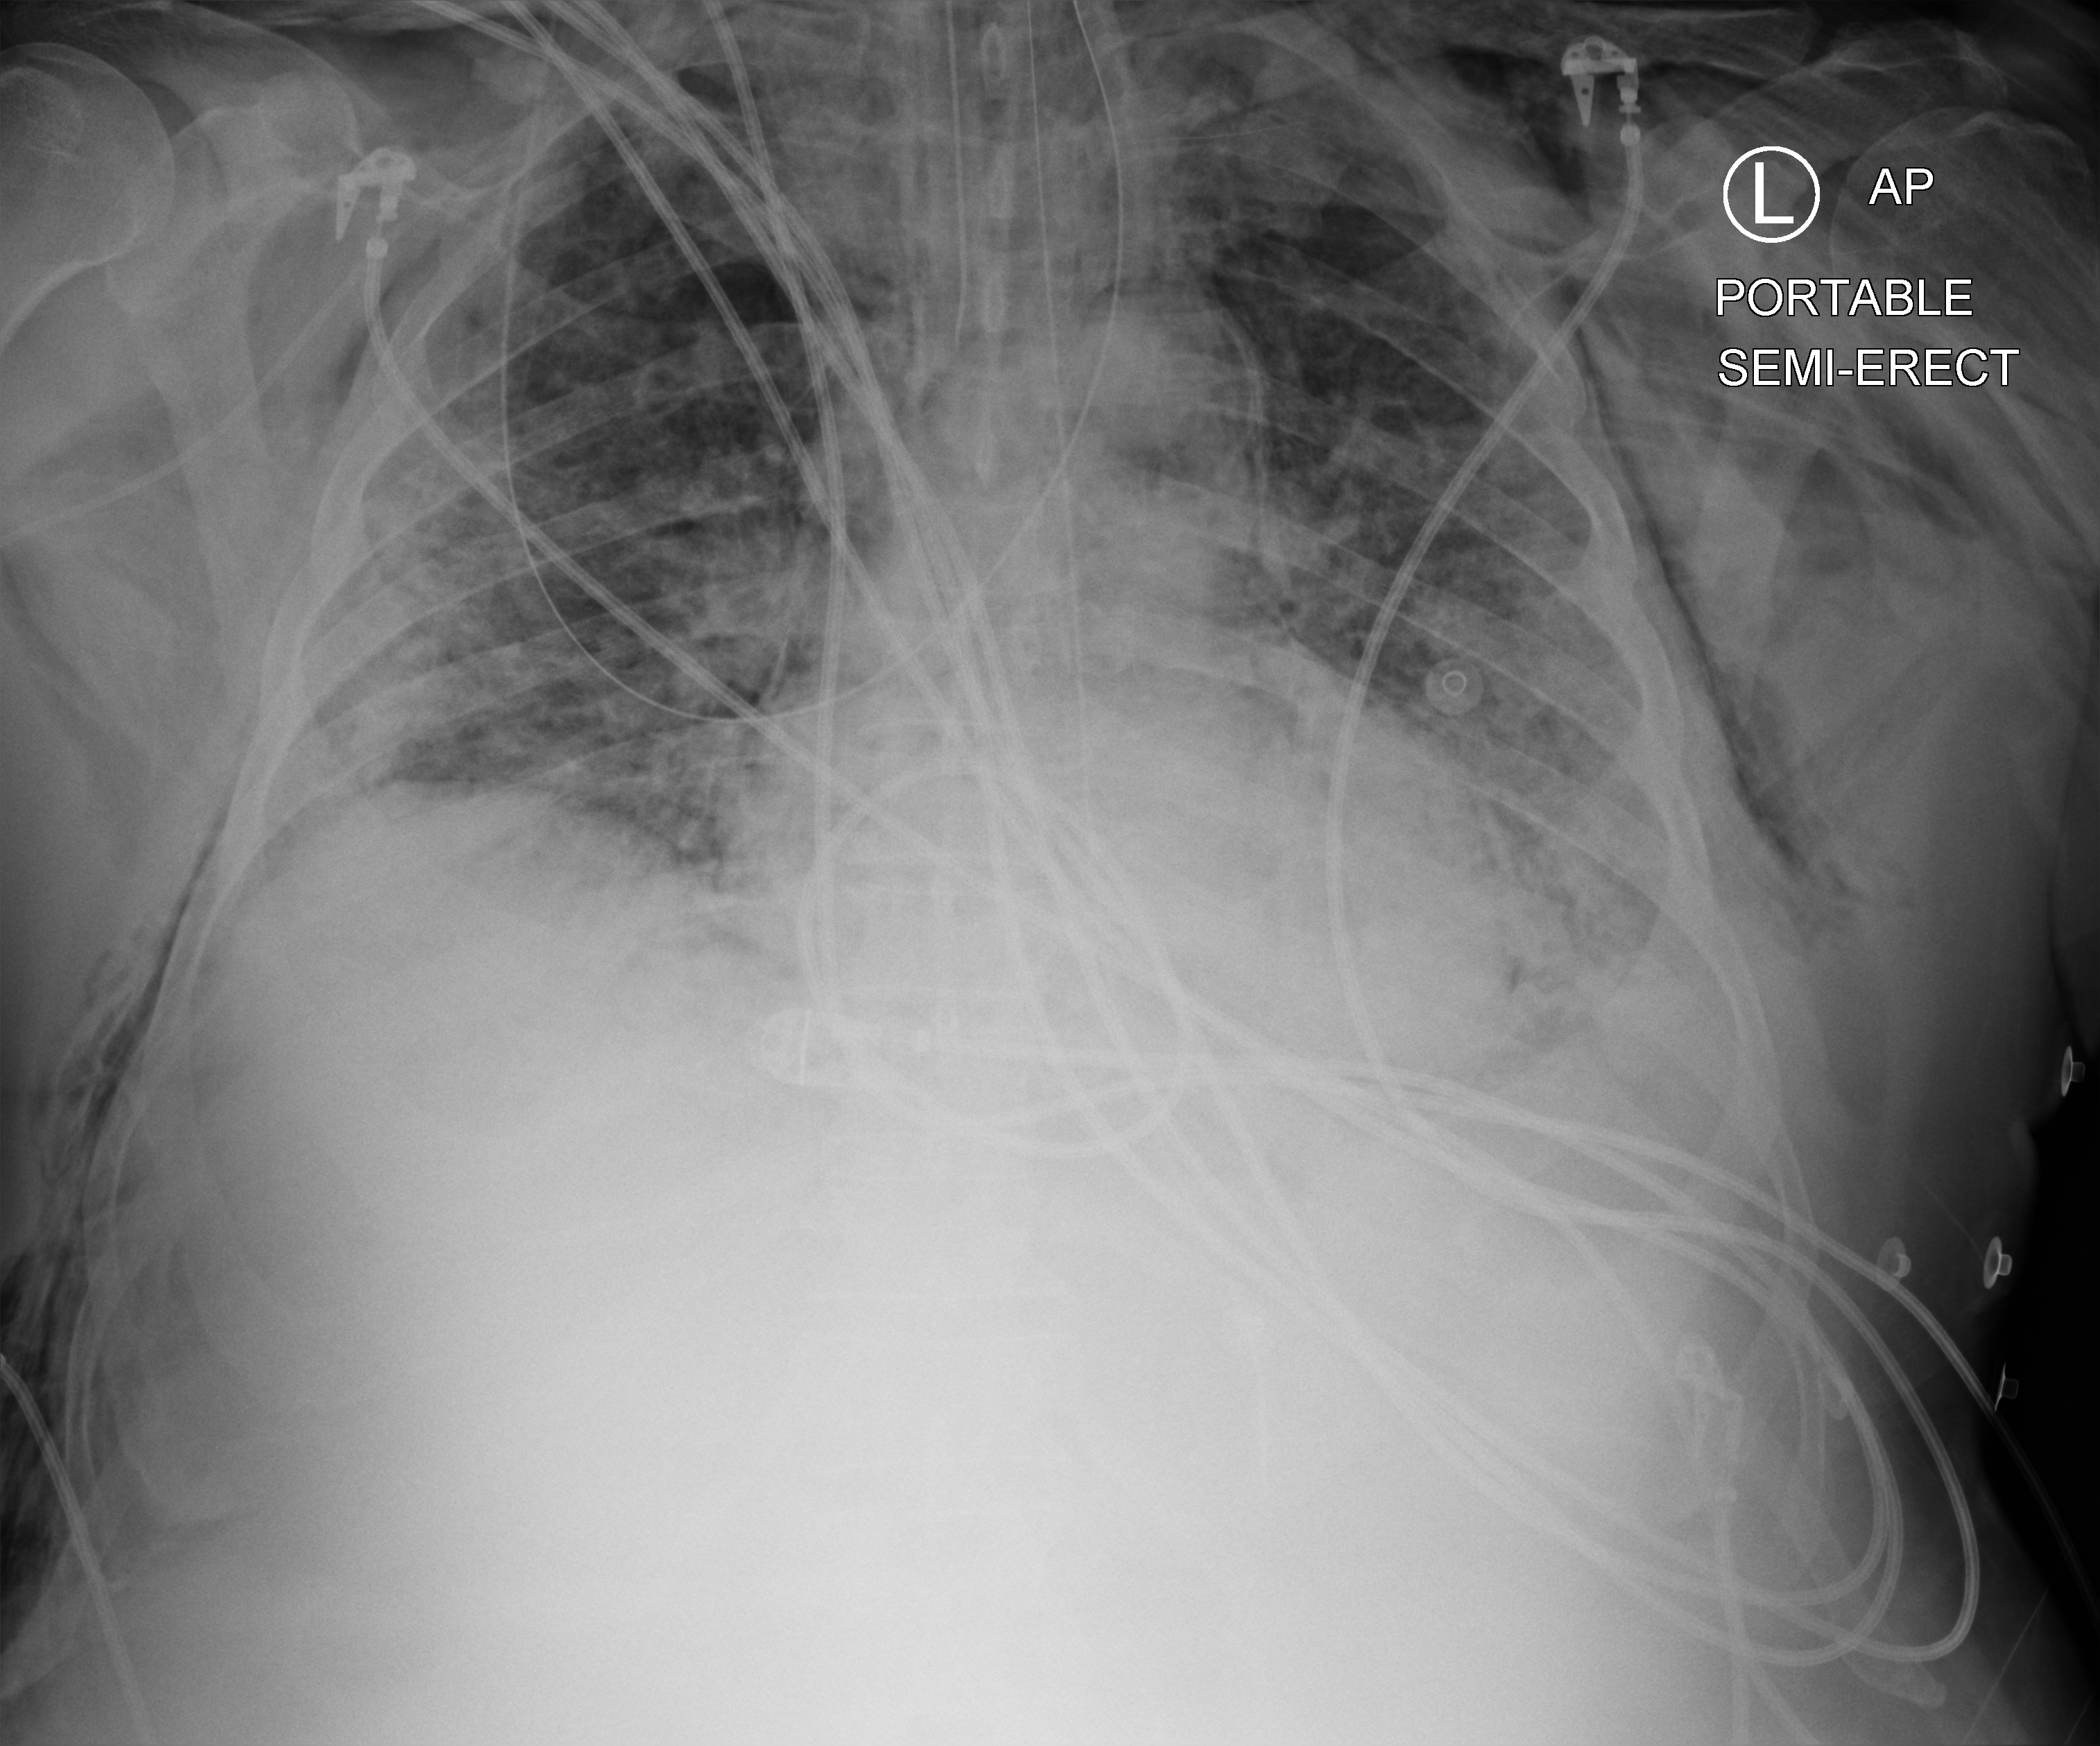
Bedside chest radiograph (computed radiography), anteroposterior (AP) projection. Patient hospitalised with COVID-19; male, aged 60–74 years.
Admission-level facts for this patient (not findings on this image; timing relative to this image not recorded):
- admitted to intensive care during this hospital stay: yes